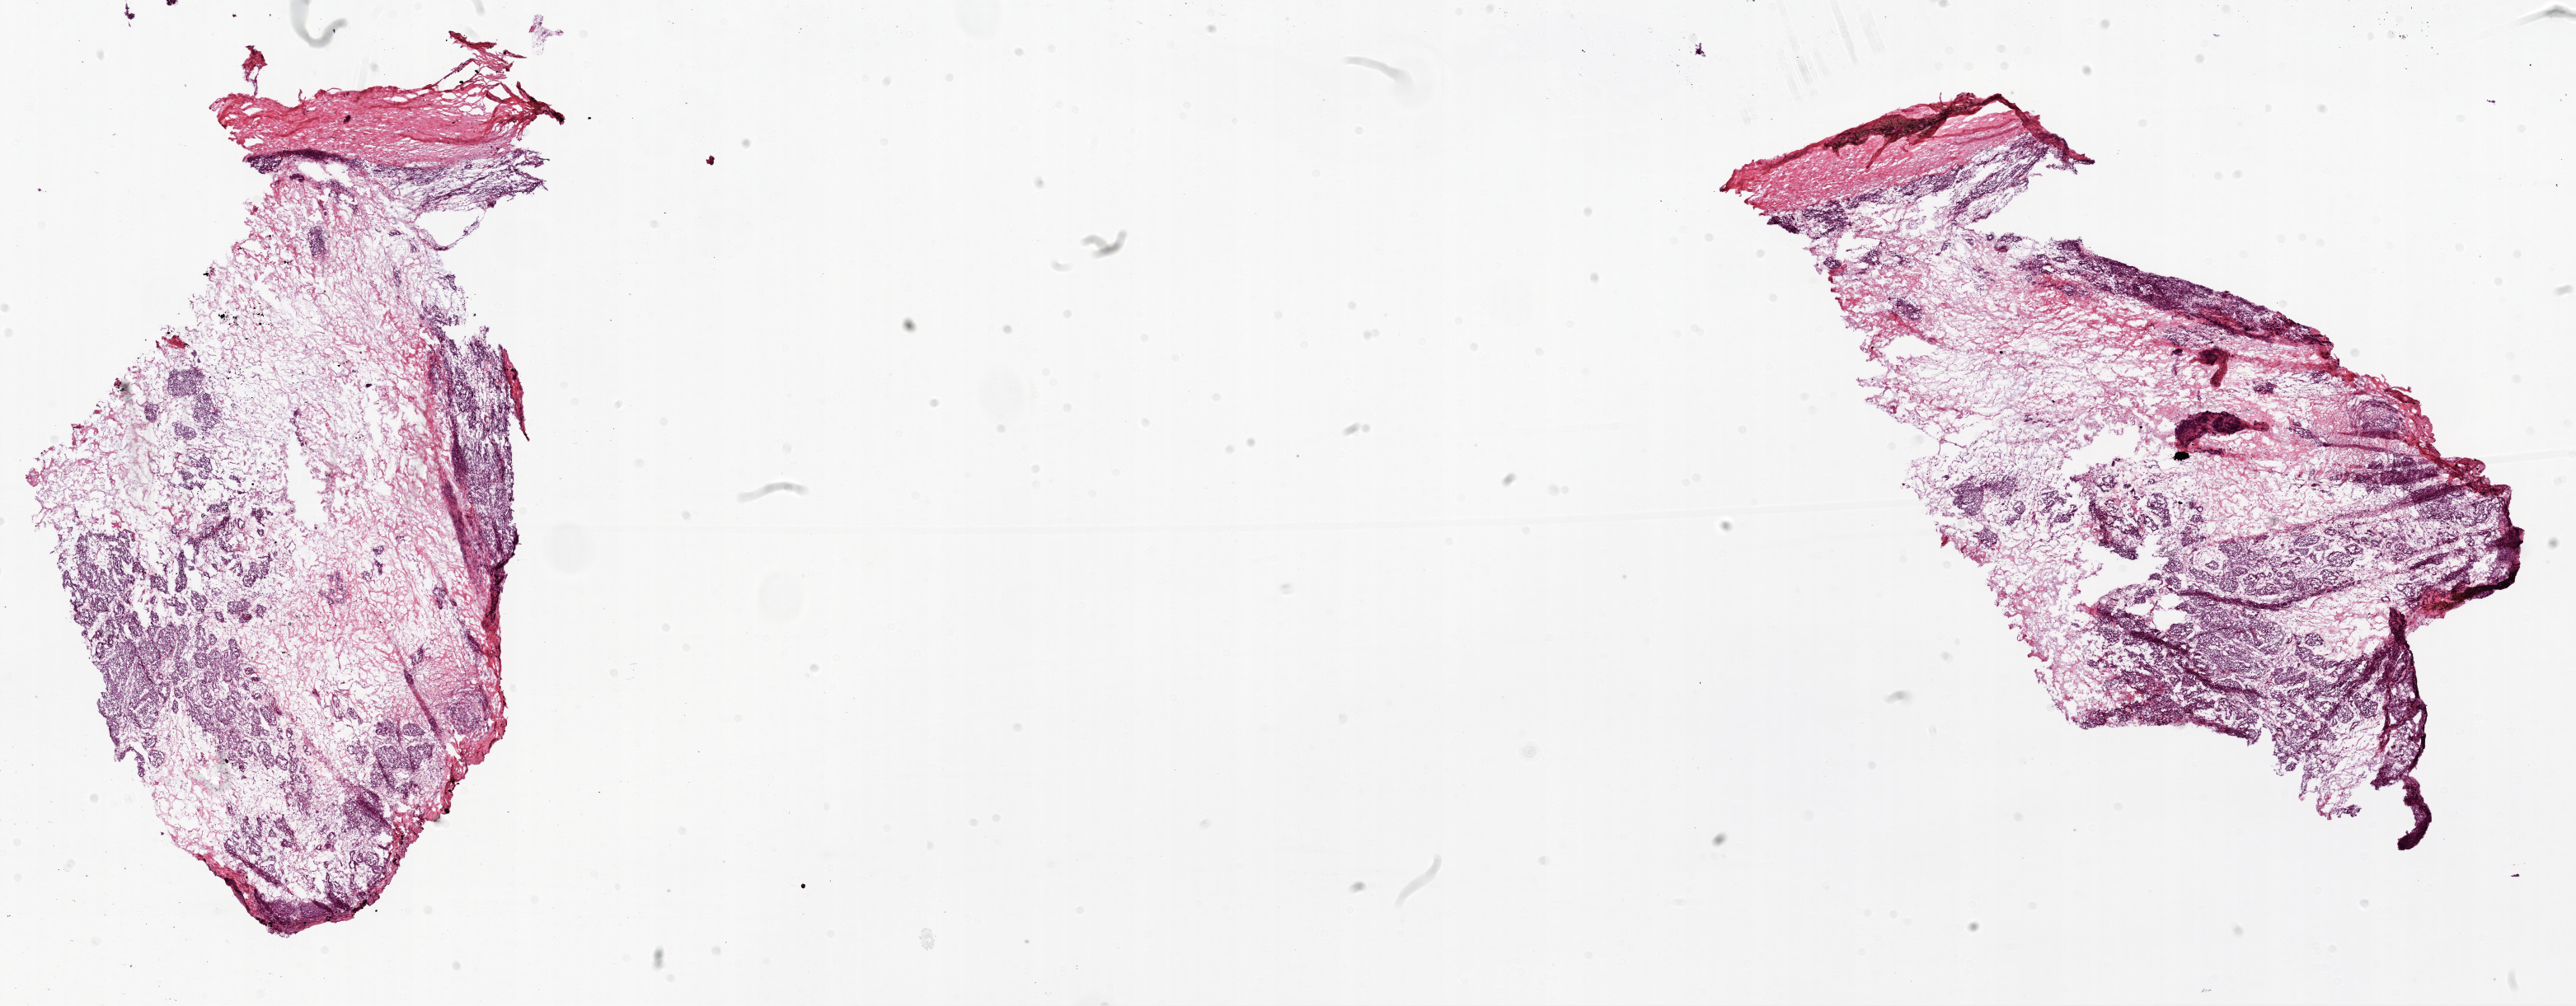
Digitized H&E tissue section (whole slide) — shown as a low-resolution overview of the whole scanned area (about 25.1 x 9.8 mm); frozen section from the top of the tissue portion; primary tumour sample from the ovary. Female patient; age at initial diagnosis 51 years.
Pathologic diagnosis: Serous cystadenocarcinoma, NOS.